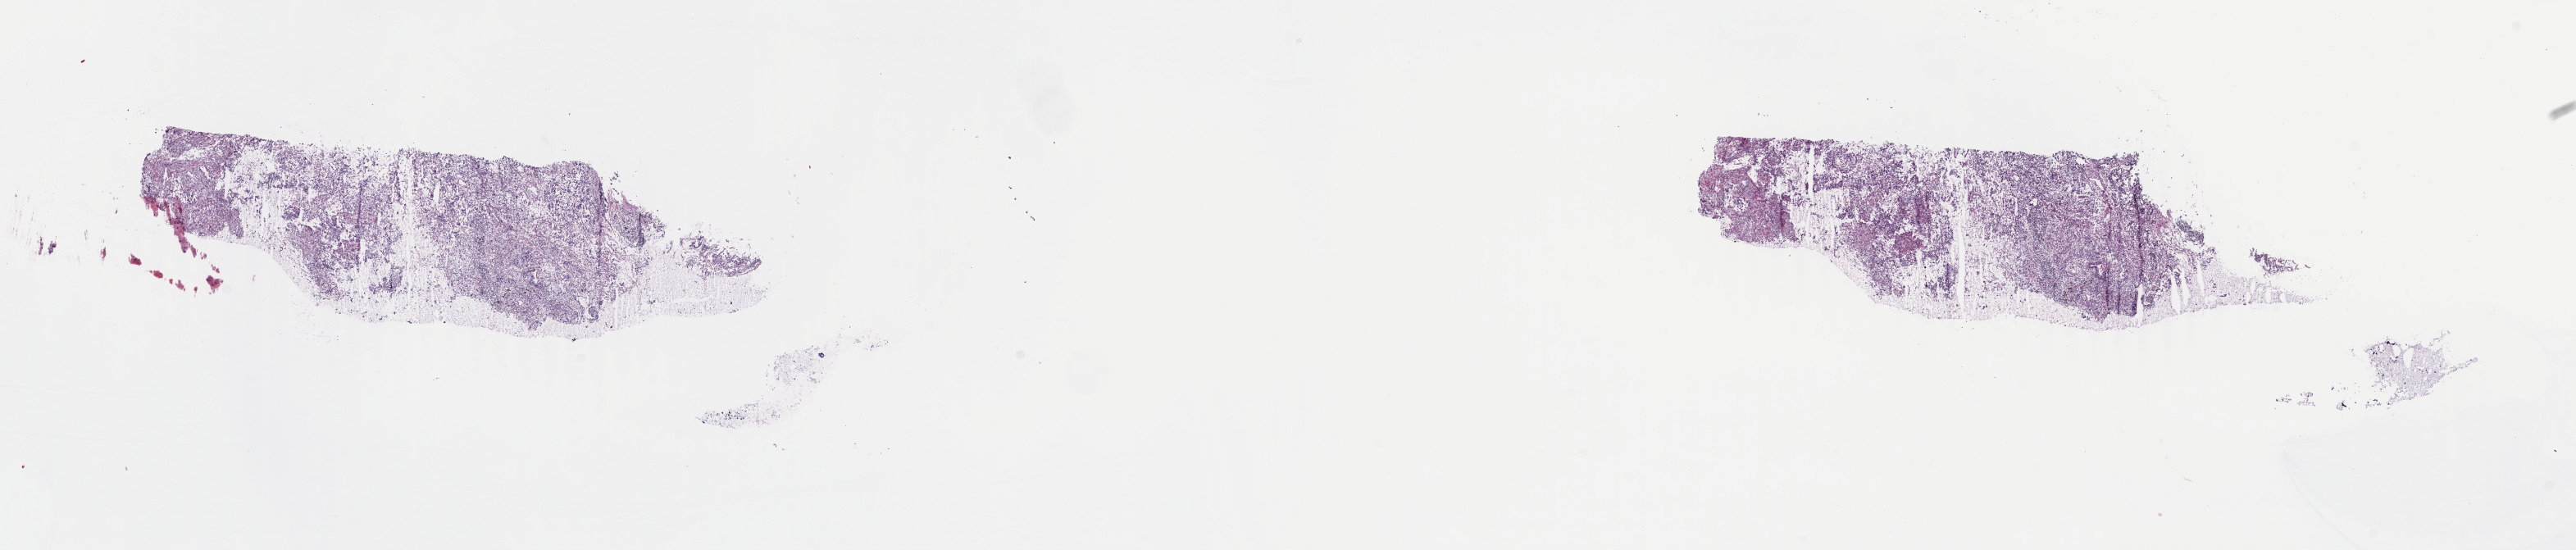
Digitized Hematoxylin and eosin (H&E) stained tissue section (whole slide) — a low-resolution overview of the entire scanned area, about 25.0 x 5.3 mm (from a 40x scan); frozen section from the top of the tissue portion; sample: primary tumour, lung. Male, age 49 years at initial diagnosis. Slide review estimates, as recorded: tumour cells 75%, tumour nuclei 75%, normal cells 0%, stromal cells 25%, necrosis 0%. Infiltration values recorded for this section: lymphocyte infiltration 5%, monocyte infiltration 2%, neutrophil infiltration 2%.
• AJCC pathologic stage: IA (7th edition)
• diagnosis: Acinar cell carcinoma (upper lobe, lung)
• TNM: T1b N0 MX